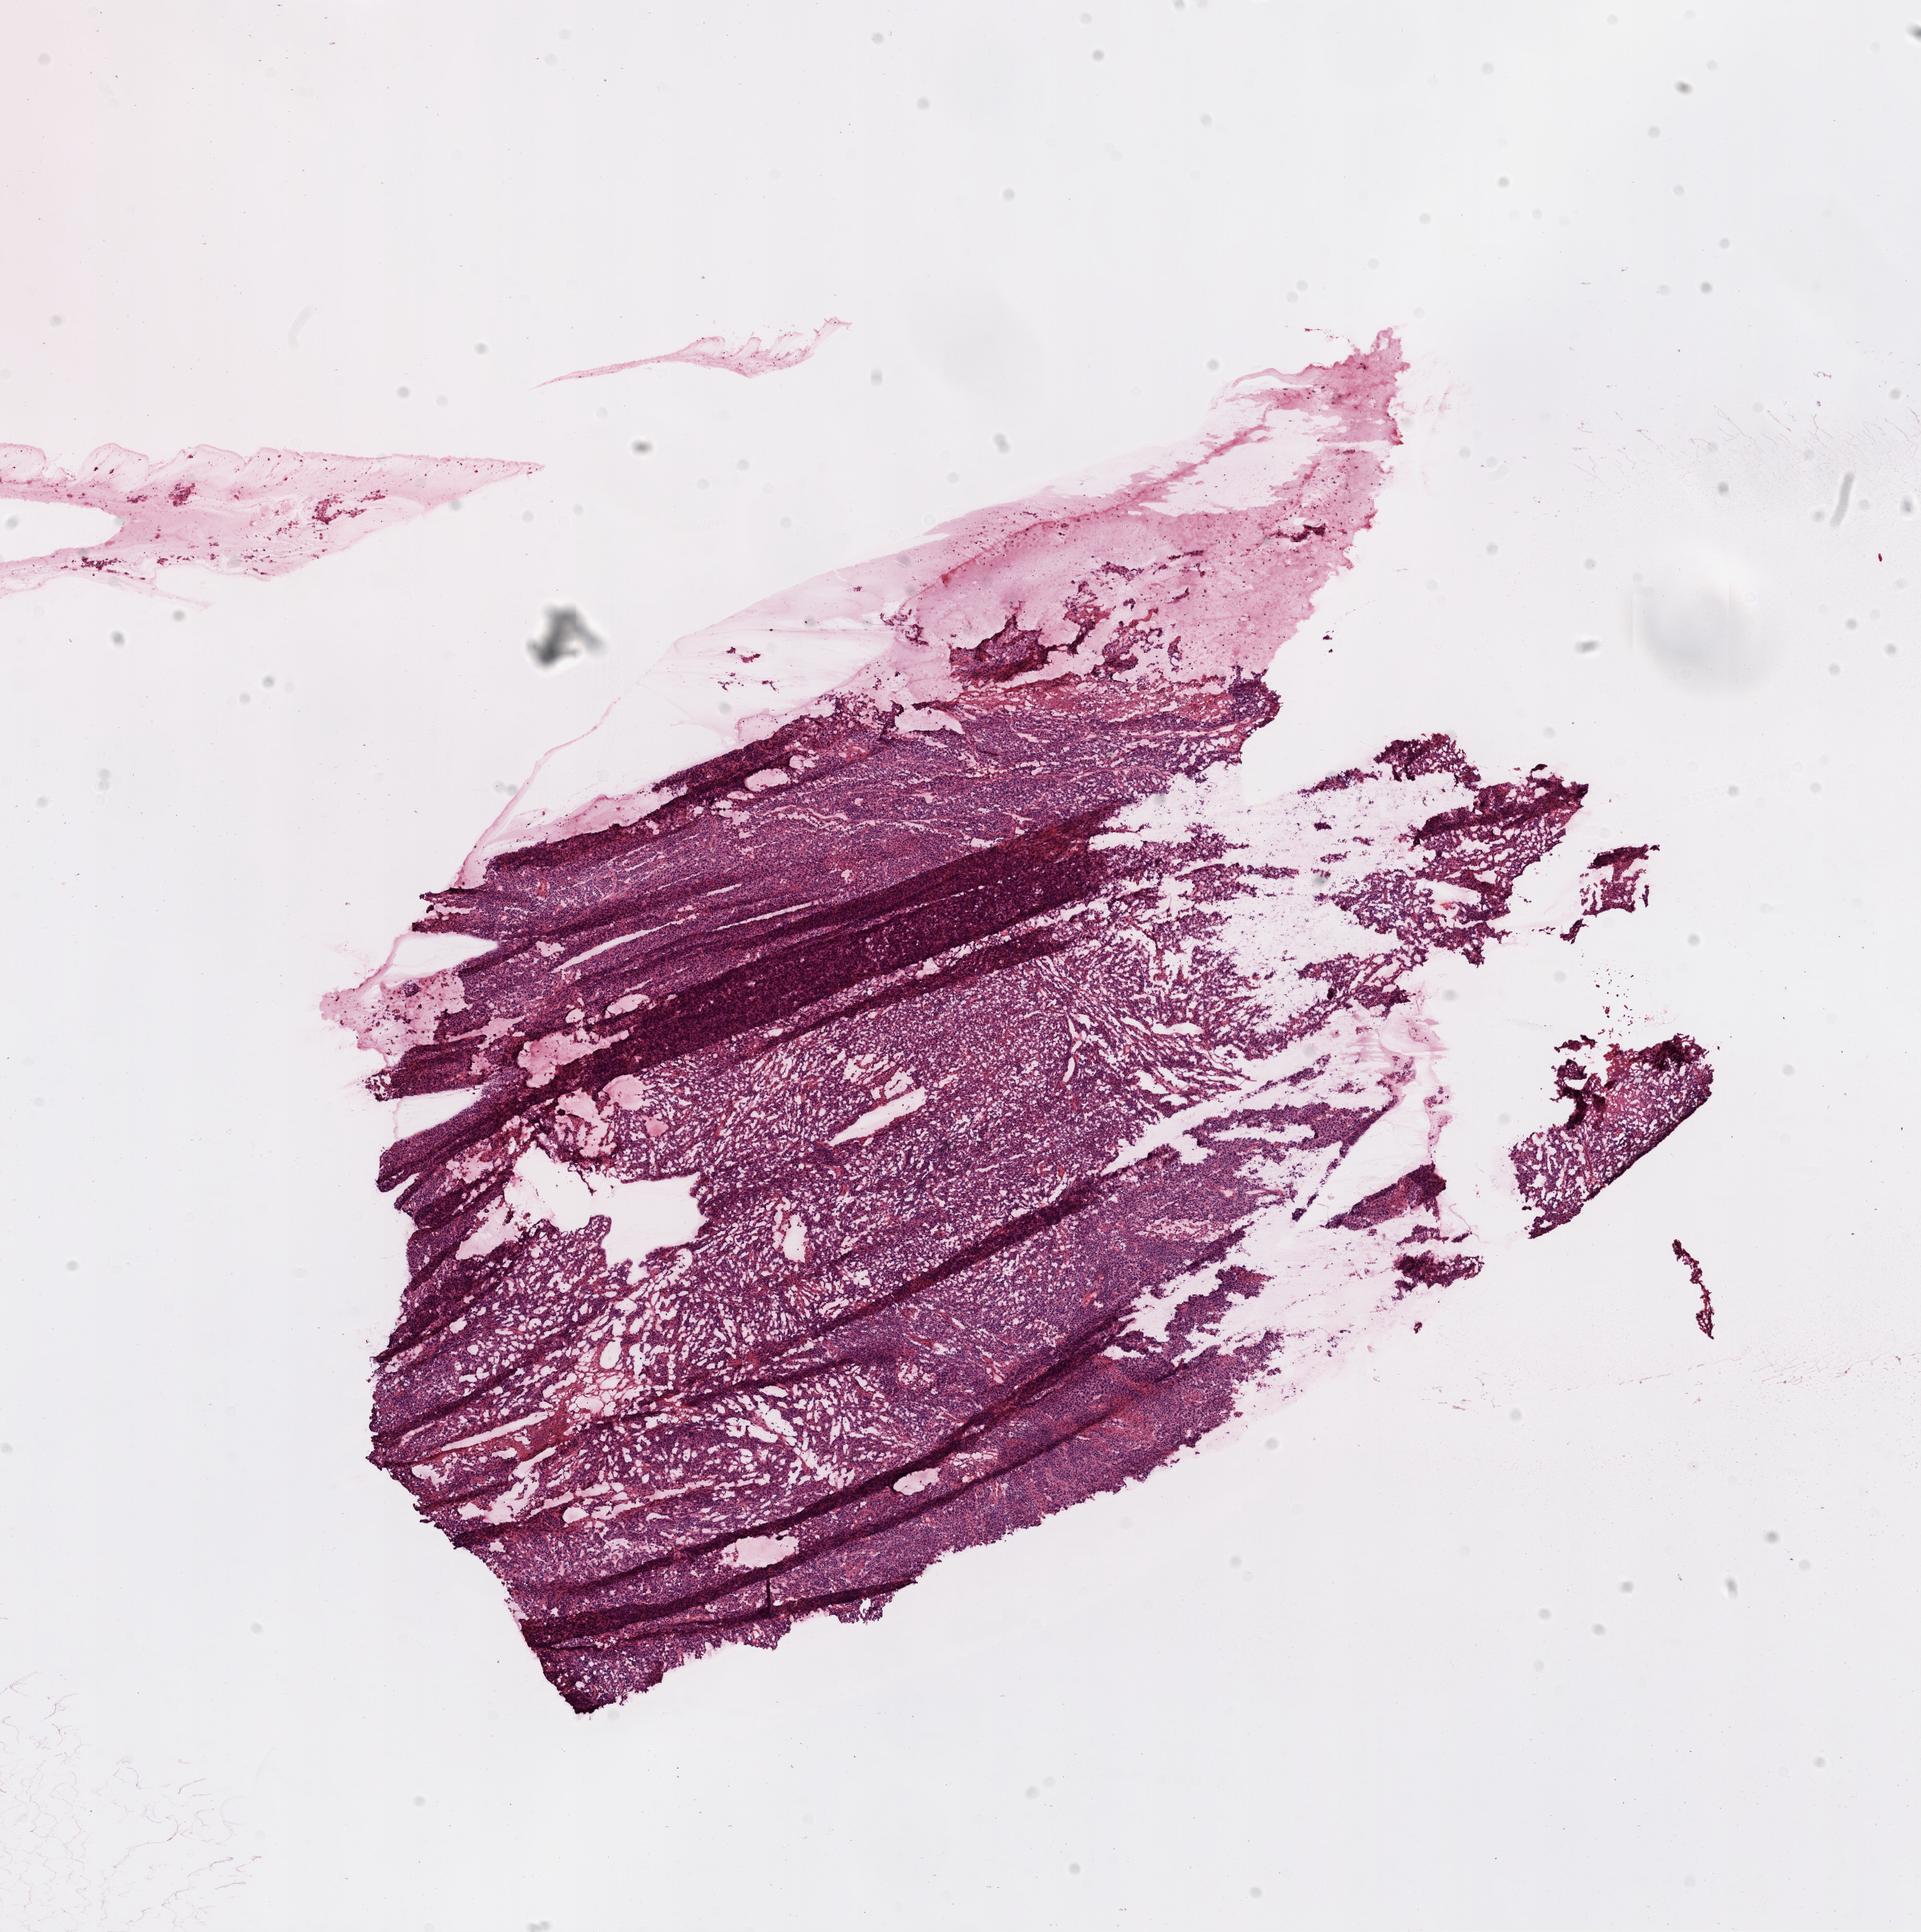
Whole-slide histology image, H&E-stained — whole scanned area (about 9.7 x 9.7 mm) shown as a low-resolution overview; frozen section; ovary, primary tumour sample. Patient: female, age at initial diagnosis 78 years. Histologic grade: G3 (poorly differentiated). Pathologist review of this section (percent, as recorded): tumour cells 96%, tumour nuclei 98%, normal cells 2%, stromal cells 0%, necrosis 2%.
Diagnosis: Serous cystadenocarcinoma, NOS. FIGO stage: IIB.